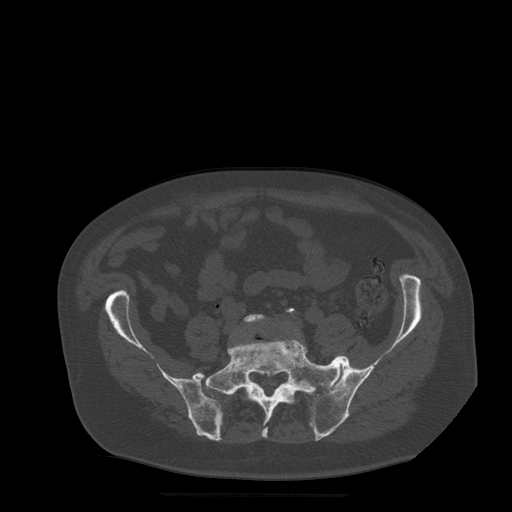
CT including the spine, one axial slice. Position 69 of 522 along the scan axis. Bone window (W 1800 / L 400 HU). 1.25 mm slice thickness. 512 × 512 image matrix, field of view 420 × 420 mm. Patient age 72 years. From the clinical record (not read from this slice): primary cancer: prostate.
Annotated regions visible in this slice (semi-automatically segmented with operator editing):
- L5 vertebra: bounding box (x1, y1, x2, y2) in pixels: (243, 314, 266, 392)